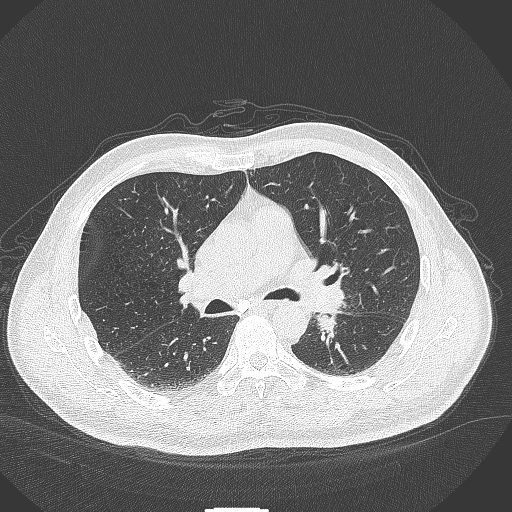
Chest CT, one axial slice. Position 245 of 429 along the scan axis. 120 kVp. Lung window (W 1500 / L -600 HU). 512 × 512 image matrix, field of view 400 × 400 mm. Patient: male, 55 years. Case-level facts recorded for this patient, not image findings: clinical TNM (as recorded): T3 N0 M1c; histopathological grade: G3.
Outlined on this slice (rectangle marked by the reading radiologist):
- lung tumour (recorded histology: adenocarcinoma): bounding box <311,303,345,342> (left, top, right, bottom; pixels)